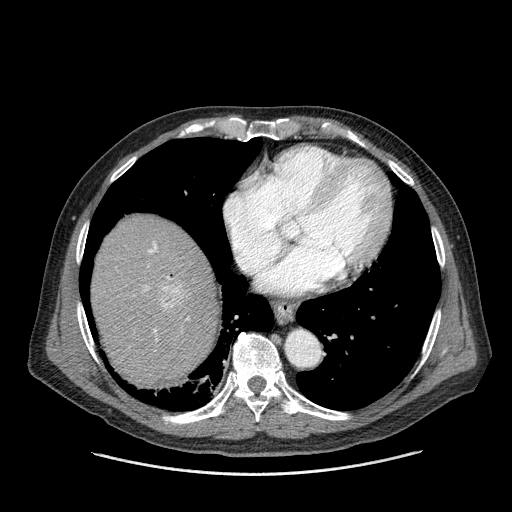
Contrast-enhanced abdominal CT (liver protocol), one axial slice; position 142 of 180 along the scan axis; 120 kVp; one of 2 acquisitions stored at this slice position; soft-tissue window (W 400 / L 40 HU); 512 × 512 image matrix, field of view 420 × 420 mm. From the clinical record (not read from this slice): diagnosis: hepatocellular carcinoma (patient treated with transarterial chemoembolisation; whether this scan precedes or follows treatment is not stated here); TNM stage (as recorded): Stage-II; Child-Pugh class: A; tumour nodularity: multinodular.
Annotated regions visible in this slice (semi-automatic segmentation, software-assisted and operator-edited):
- abdominal aorta: box from (x=288, y=333) to (x=319, y=366) px
- liver parenchyma outside the tumour (the mass and vessels are separate outlines, so this box may not span the whole liver): (x=92, y=214)–(x=218, y=386)
- mass: (x=158, y=284)–(x=186, y=309)
- liver vessels: (x=145, y=242)–(x=188, y=341)